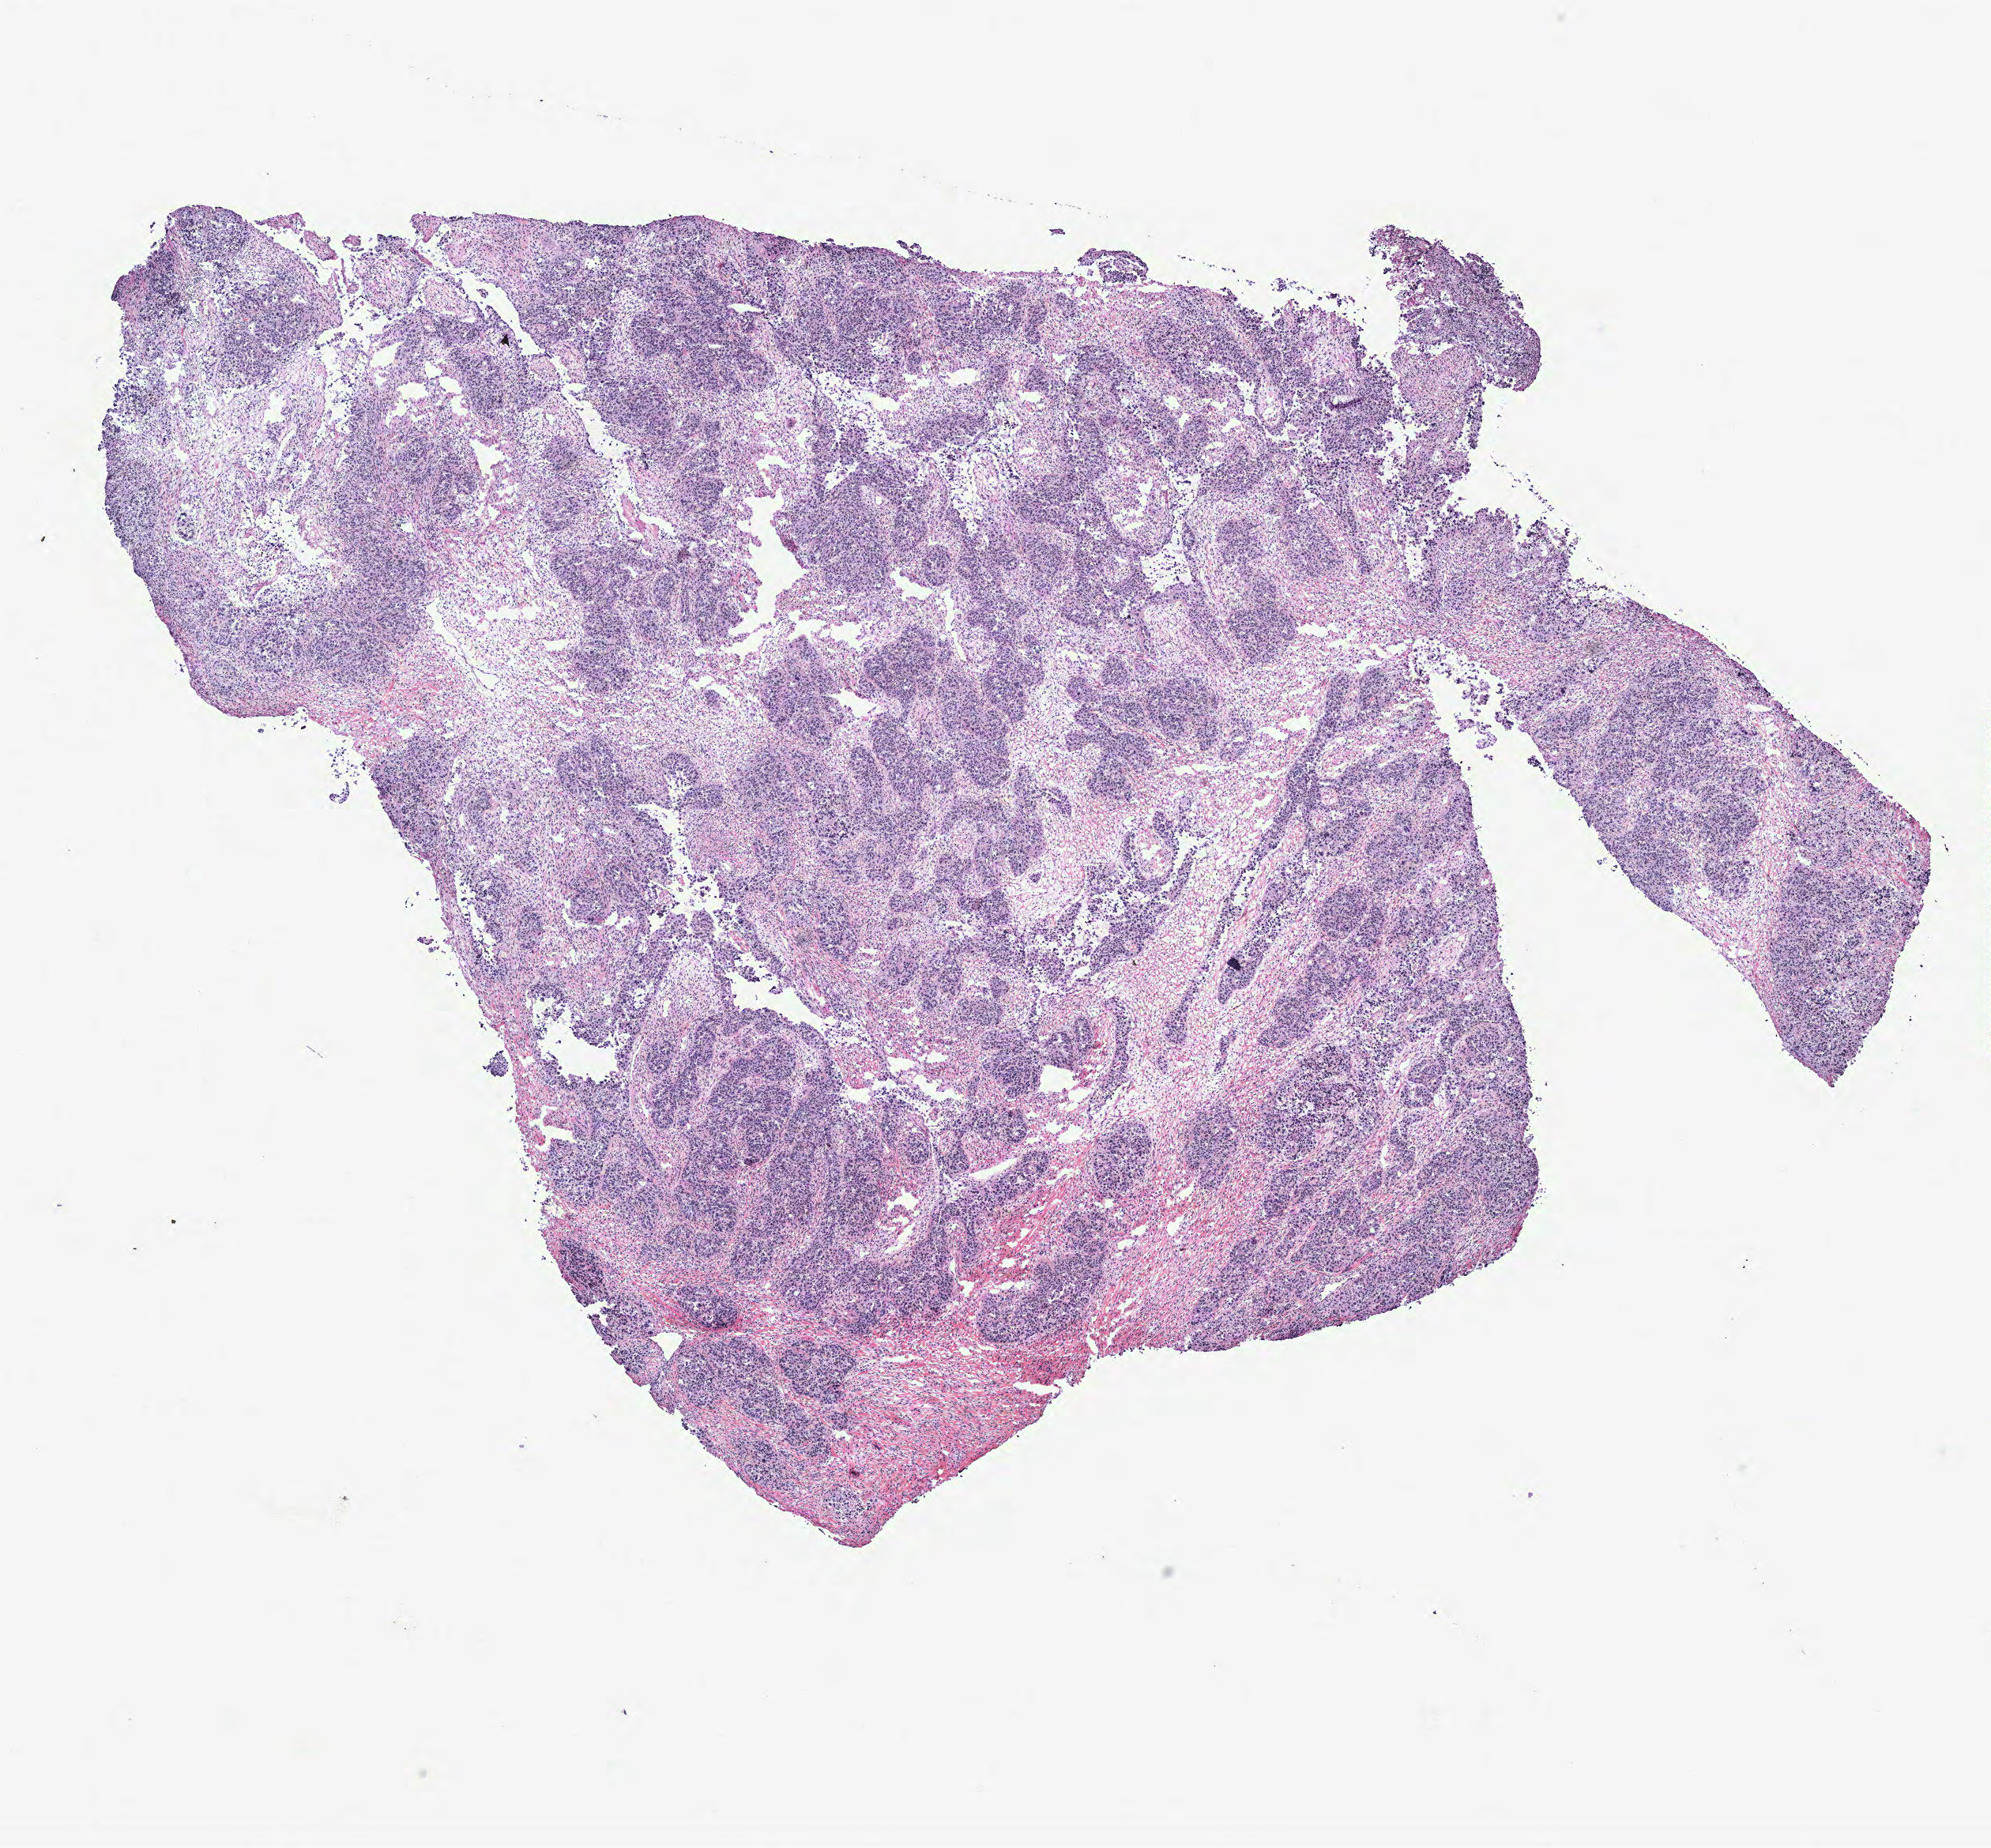
Digitized H&E-stained tissue section (whole slide) — shown as a low-resolution overview of the whole scanned area (about 10.1 x 9.4 mm, from a 40x scan); ovary, tissue type not recorded.
Patient diagnosis (cohort enrolment): ovarian cancer (ovary).